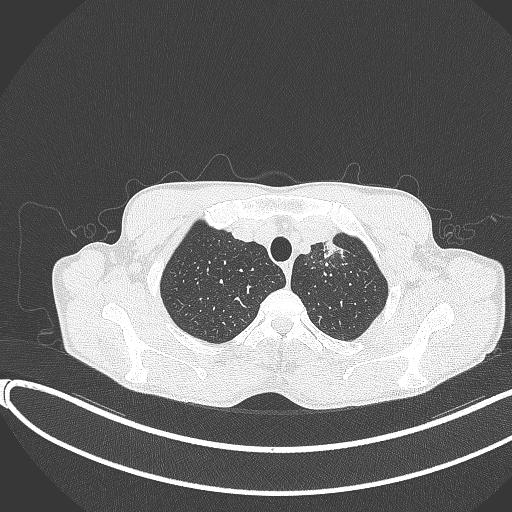
Chest CT, one axial slice; position 335 of 374 along the scan axis; reconstruction kernel B70f; lung window (W 1500 / L -600 HU); 512 × 512 image matrix. Male patient, age 58 years. From the clinical record (not read from this slice): clinical TNM (as recorded): T1c N1 M0.
Annotated regions visible in this slice (rectangle marked by the reading radiologist):
- lung tumour (recorded histology: adenocarcinoma): bounding box [x1, y1, x2, y2] px = [312, 235, 346, 269]